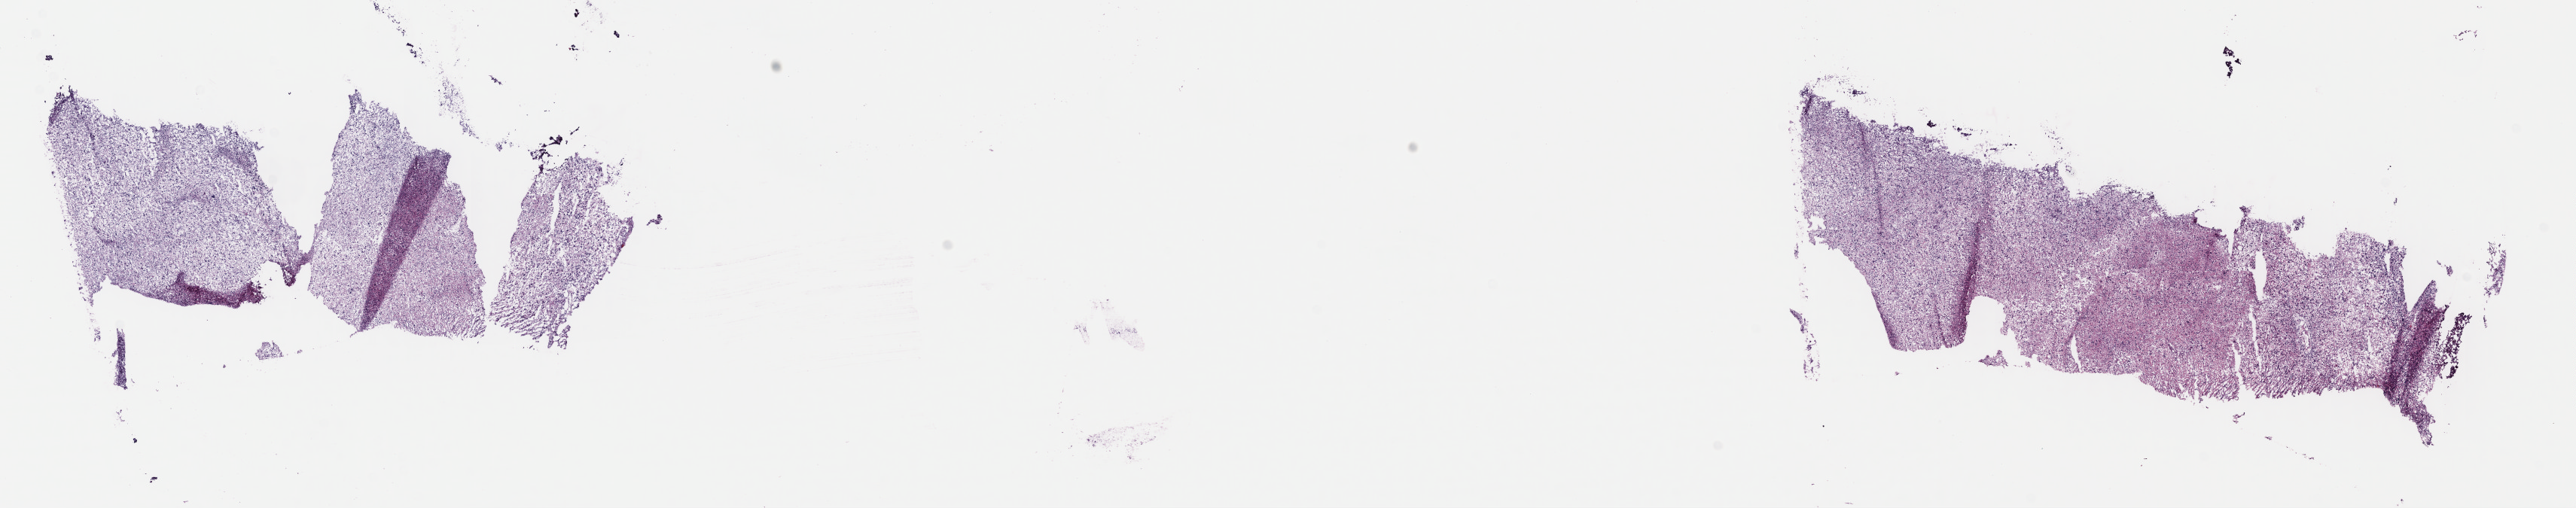
H&E-stained whole-slide image, low-resolution overview of the scanned area, about 26.9 x 5.3 mm (from a 40x scan); frozen section from the top of the tissue portion; sample: recurrent tumour, brain. Female patient; age at initial diagnosis 35 years. Pathologist review of this section (percent, as recorded): tumour cells 50%, tumour nuclei 85%, normal cells 5%, stromal cells 45%, necrosis 0%. Inflammatory infiltration, as recorded: lymphocyte infiltration 0%, monocyte infiltration 0%, neutrophil infiltration 0%.
• this section: recurrent tumour
• patient diagnosis: Oligodendroglioma, NOS (cerebrum)